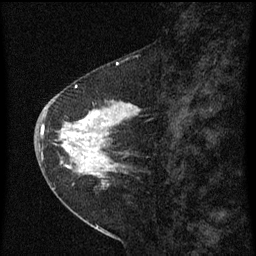
Breast MRI (dynamic contrast-enhanced), one sagittal slice; slice 25 of 60 in the series (ordered by position); dynamic contrast-enhanced series, image 2 of 3 at this slice position (ordered by acquisition); 1.5 T; TE 4.2 ms, TR 8 ms; 2 mm slice thickness; 256 × 256 image matrix, field of view 180 × 180 mm. Female patient, age 47 years.
Structures marked on this image (semi-automatic segmentation, software-assisted and operator-edited):
- analysis volume of interest (the breast-tissue region the enhancement analysis was run in; not a lesion): bounding box [x1, y1, x2, y2] px = [44, 84, 141, 199]
- tumour enhancement mask (voxels above the 70 % enhancement threshold inside the analysis volume of interest): [44, 86, 141, 177]